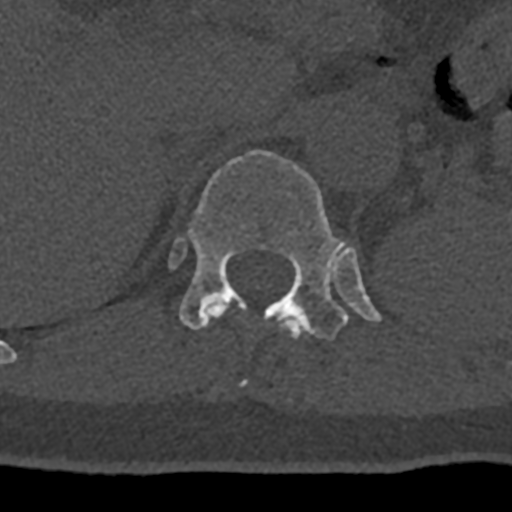
CT including the spine, one axial slice. Slice 506 of 797 in the series (ordered by position). Reconstruction kernel Br40s/3. 120 kVp. Bone window (W 1800 / L 400 HU). 0.5 mm slice thickness. 512 × 512 image matrix, field of view 160 × 160 mm. Patient: male, 74 years. Case-level facts recorded for this patient, not image findings: primary cancer: renal; vertebrae with lytic lesions (as recorded): T10, L1, L2, L3, L4, L5.
Outlined on this slice (semi-automatically segmented with operator editing):
- T11 vertebra: bounding box (x1, y1, x2, y2) in pixels: (207, 303, 304, 385)
- T12 vertebra: (169, 150, 382, 340)